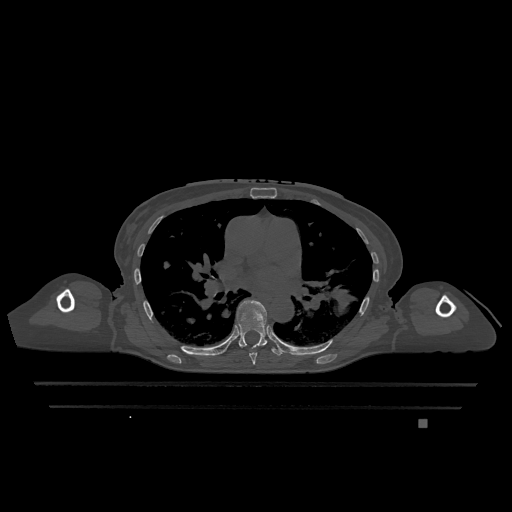
CT including the spine, one axial slice; slice 759 of 1317 in the series (ordered by position); bone window (W 1800 / L 400 HU); 512 × 512 image matrix, field of view 500 × 500 mm. Patient: female, 74 years. From the clinical record (not read from this slice): primary cancer: lung; vertebrae with lytic lesions (as recorded): T1, T4, T5, T6, L4, L5.
Outlined on this slice (semi-automatically segmented with operator editing):
- T6 vertebra: bounding box (x1, y1, x2, y2) in pixels: (241, 346, 257, 365)
- T7 vertebra: (237, 300, 282, 356)